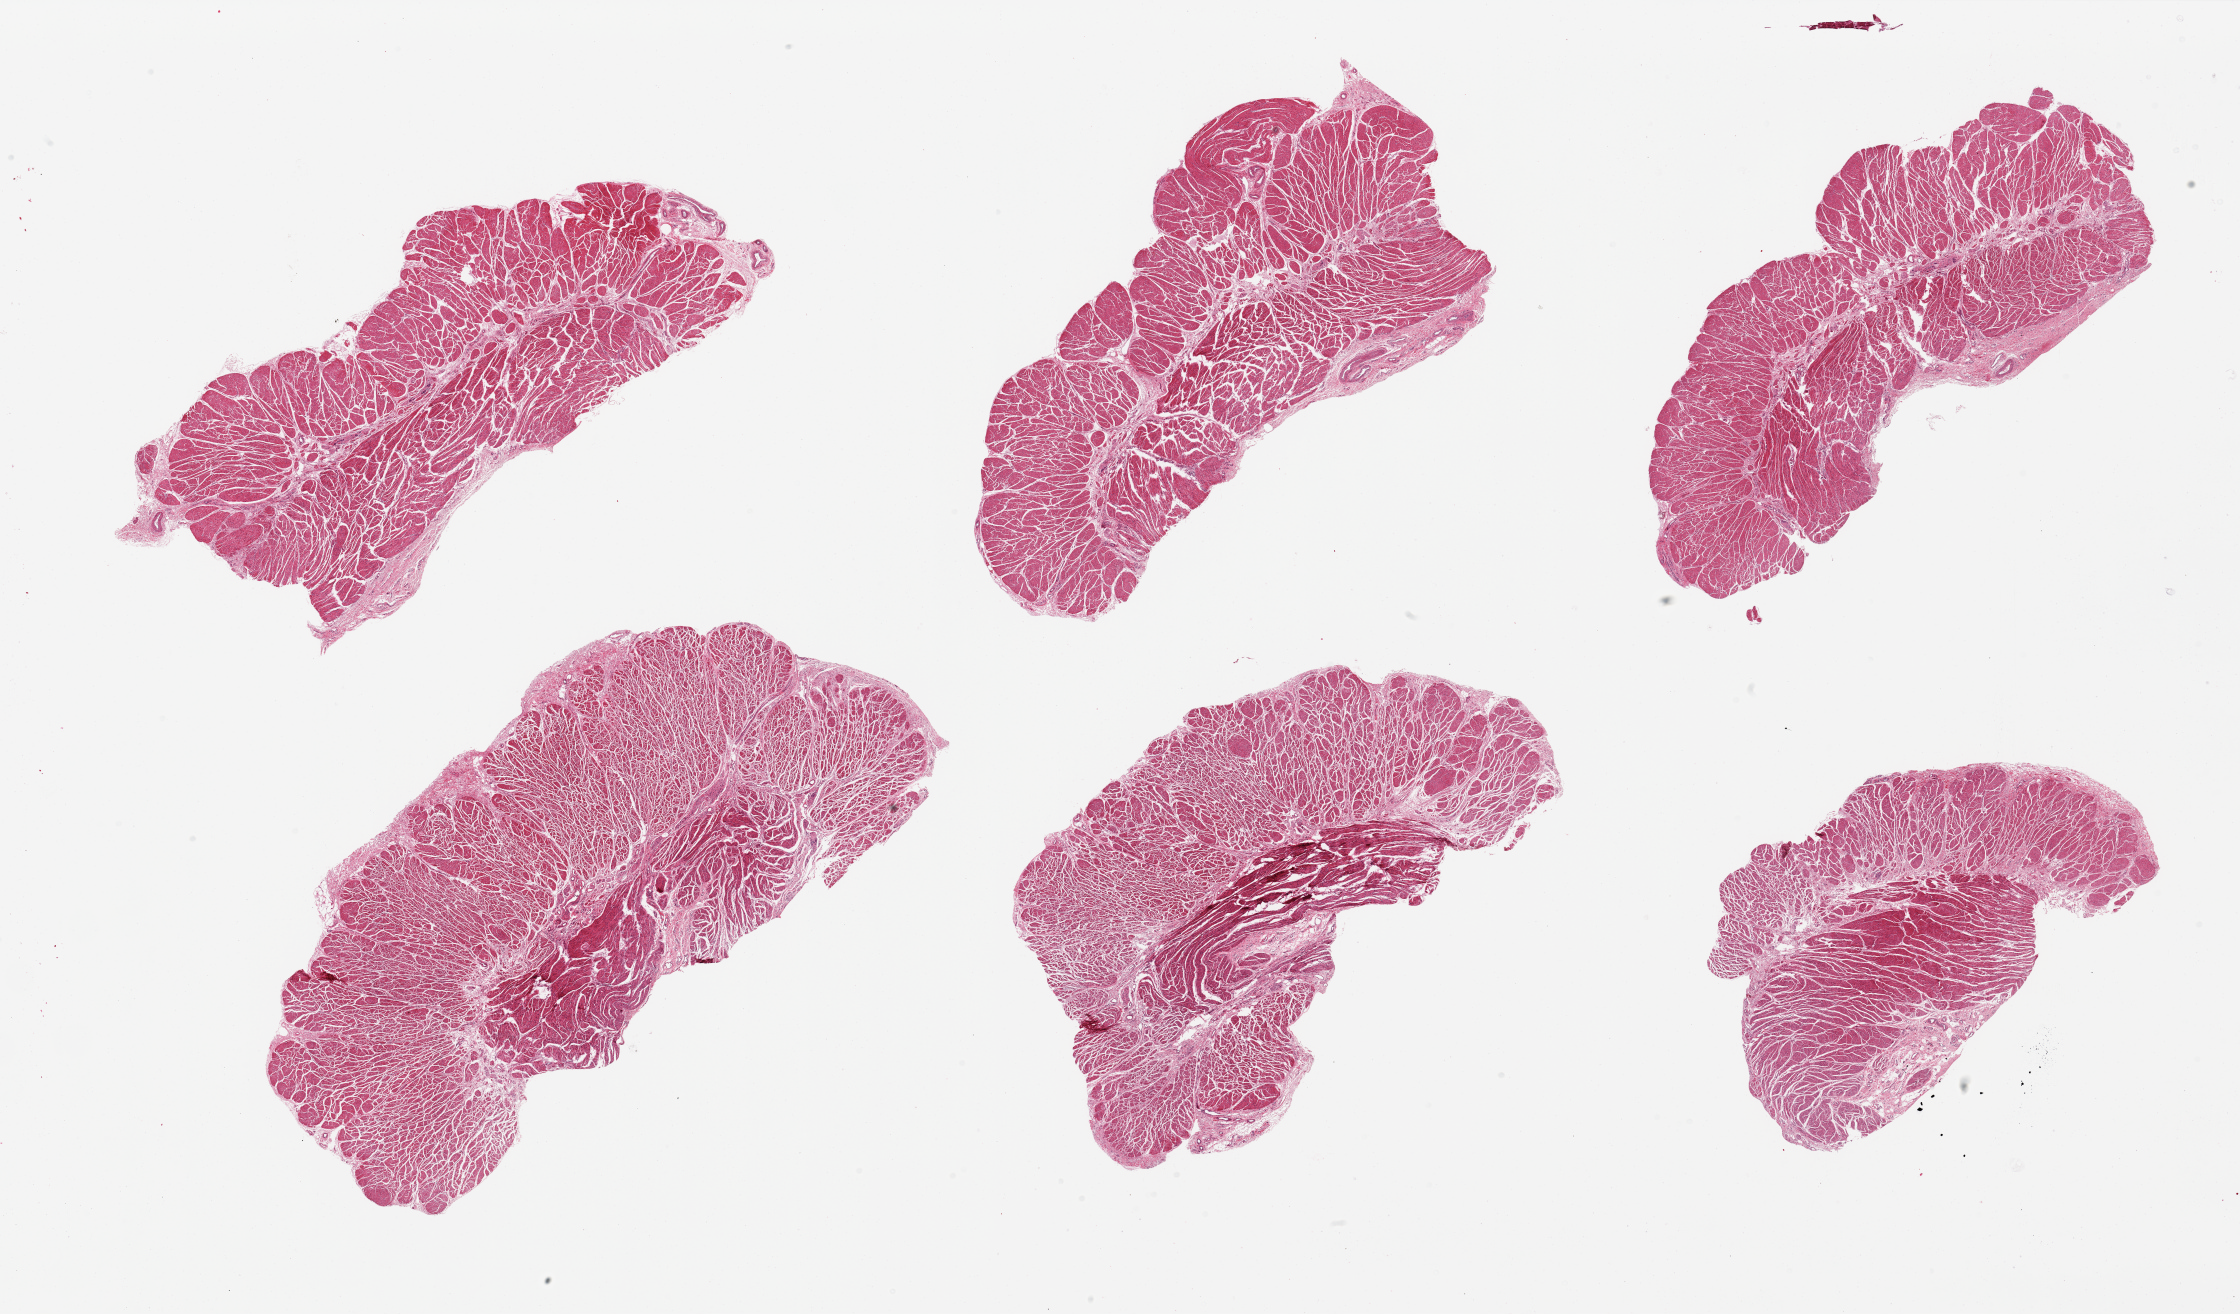
Digitized hematoxylin and eosin (H&E)-stained section, brightfield, low-resolution overview of the scanned area, about 35.4 x 20.8 mm; PAXgene-fixed paraffin-embedded (PFPE) section; target tissue: gastroesophageal junction; tissue donor sample. Female donor.
Reviewer comment on this tissue sample: 6 pieces, confirmed target muscularis.